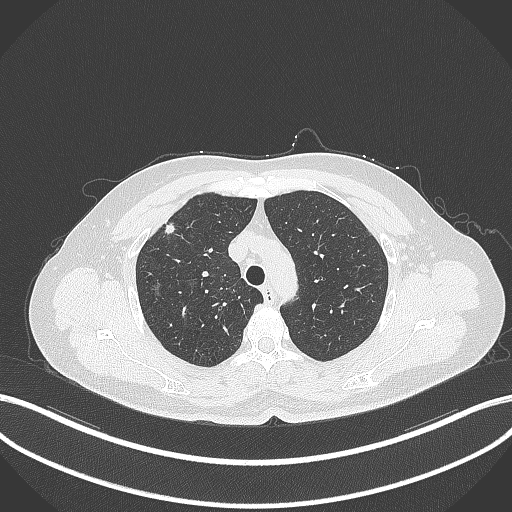
Chest CT, one axial slice; slice 283 of 353 in the series (ordered by position); reconstruction kernel B70f; lung window (W 1500 / L -600 HU); 1 mm slice thickness; 512 × 512 image matrix, field of view 400 × 400 mm. Patient: female, 56 years. From the clinical record (not read from this slice): clinical TNM (as recorded): T1c N0 M0.
Annotated regions visible in this slice (bounding box drawn by a radiologist):
- lung tumour (recorded histology: adenocarcinoma): bounding box [x1, y1, x2, y2] px = [157, 215, 183, 239]